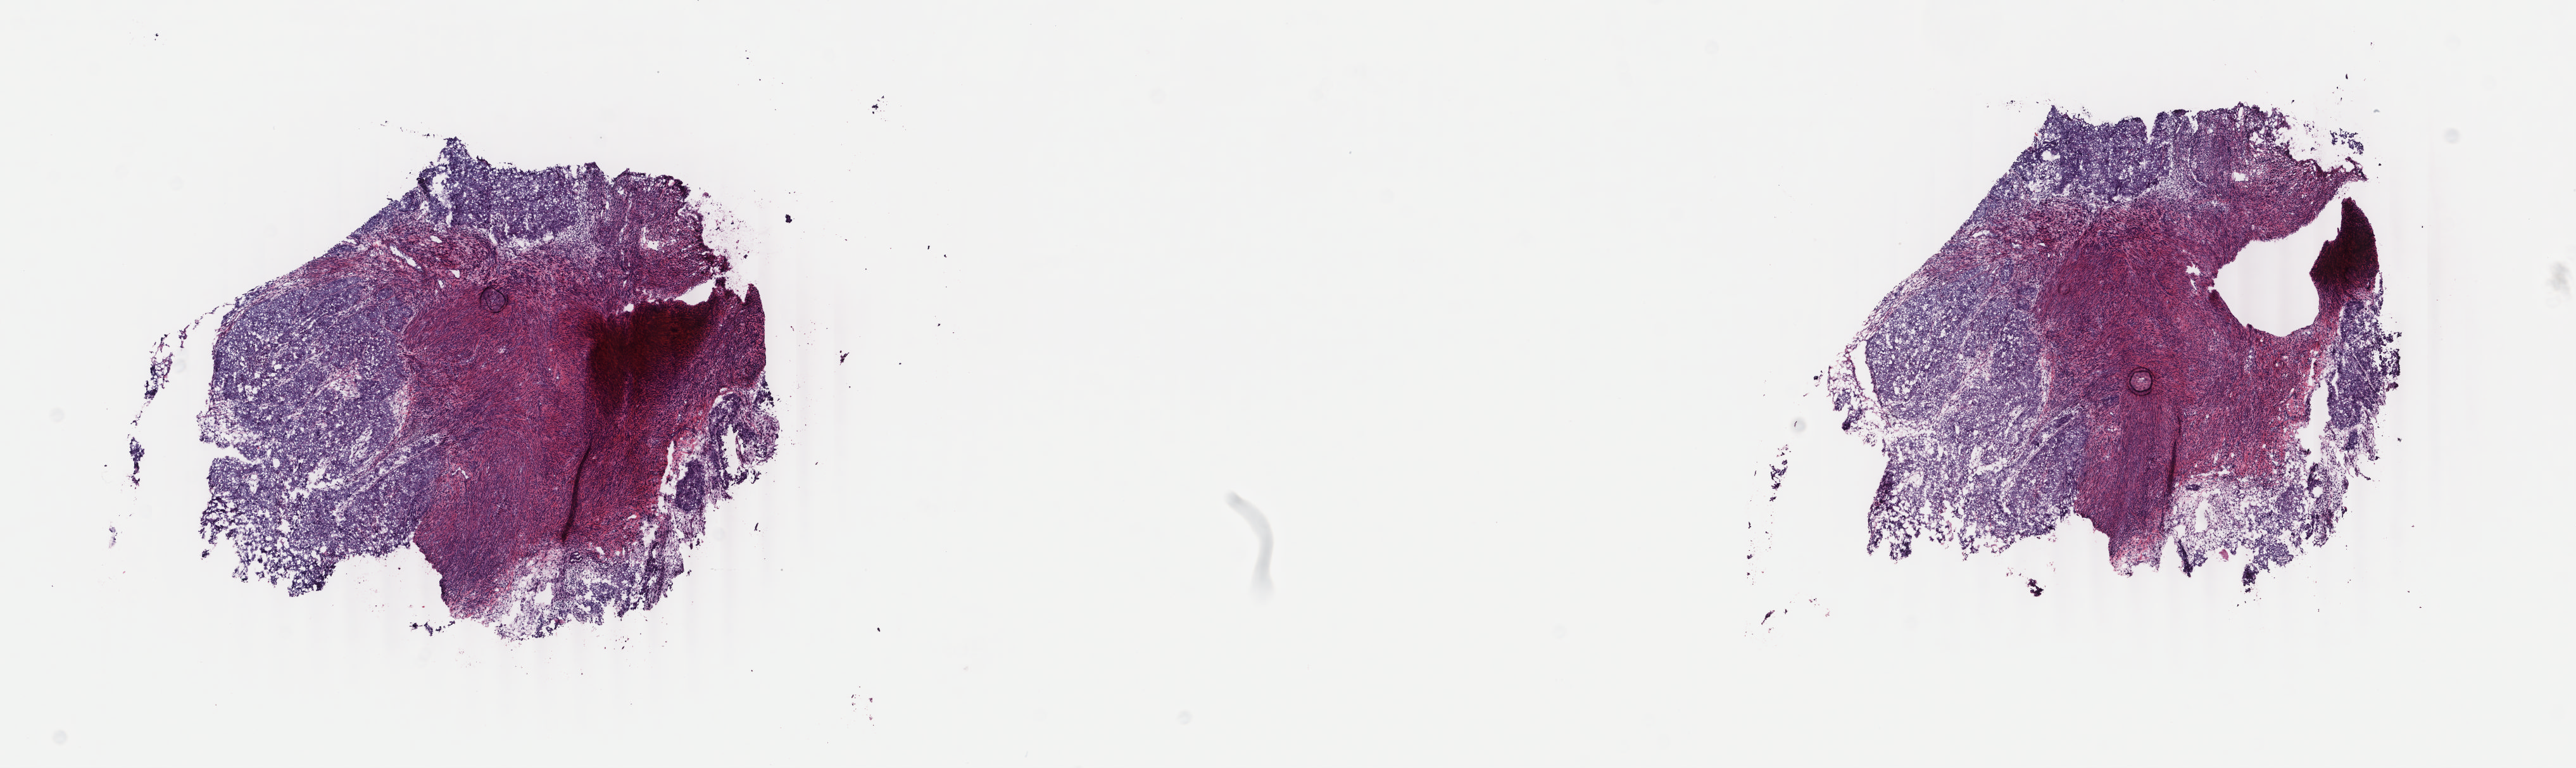
H&E whole-slide image — whole scanned area (about 16.2 x 4.8 mm, from a 40x scan) shown as a low-resolution overview. Frozen section. Primary tumour sample from the uterus. Female, age 73 years at initial diagnosis.
Diagnosis: Serous cystadenocarcinoma, NOS.